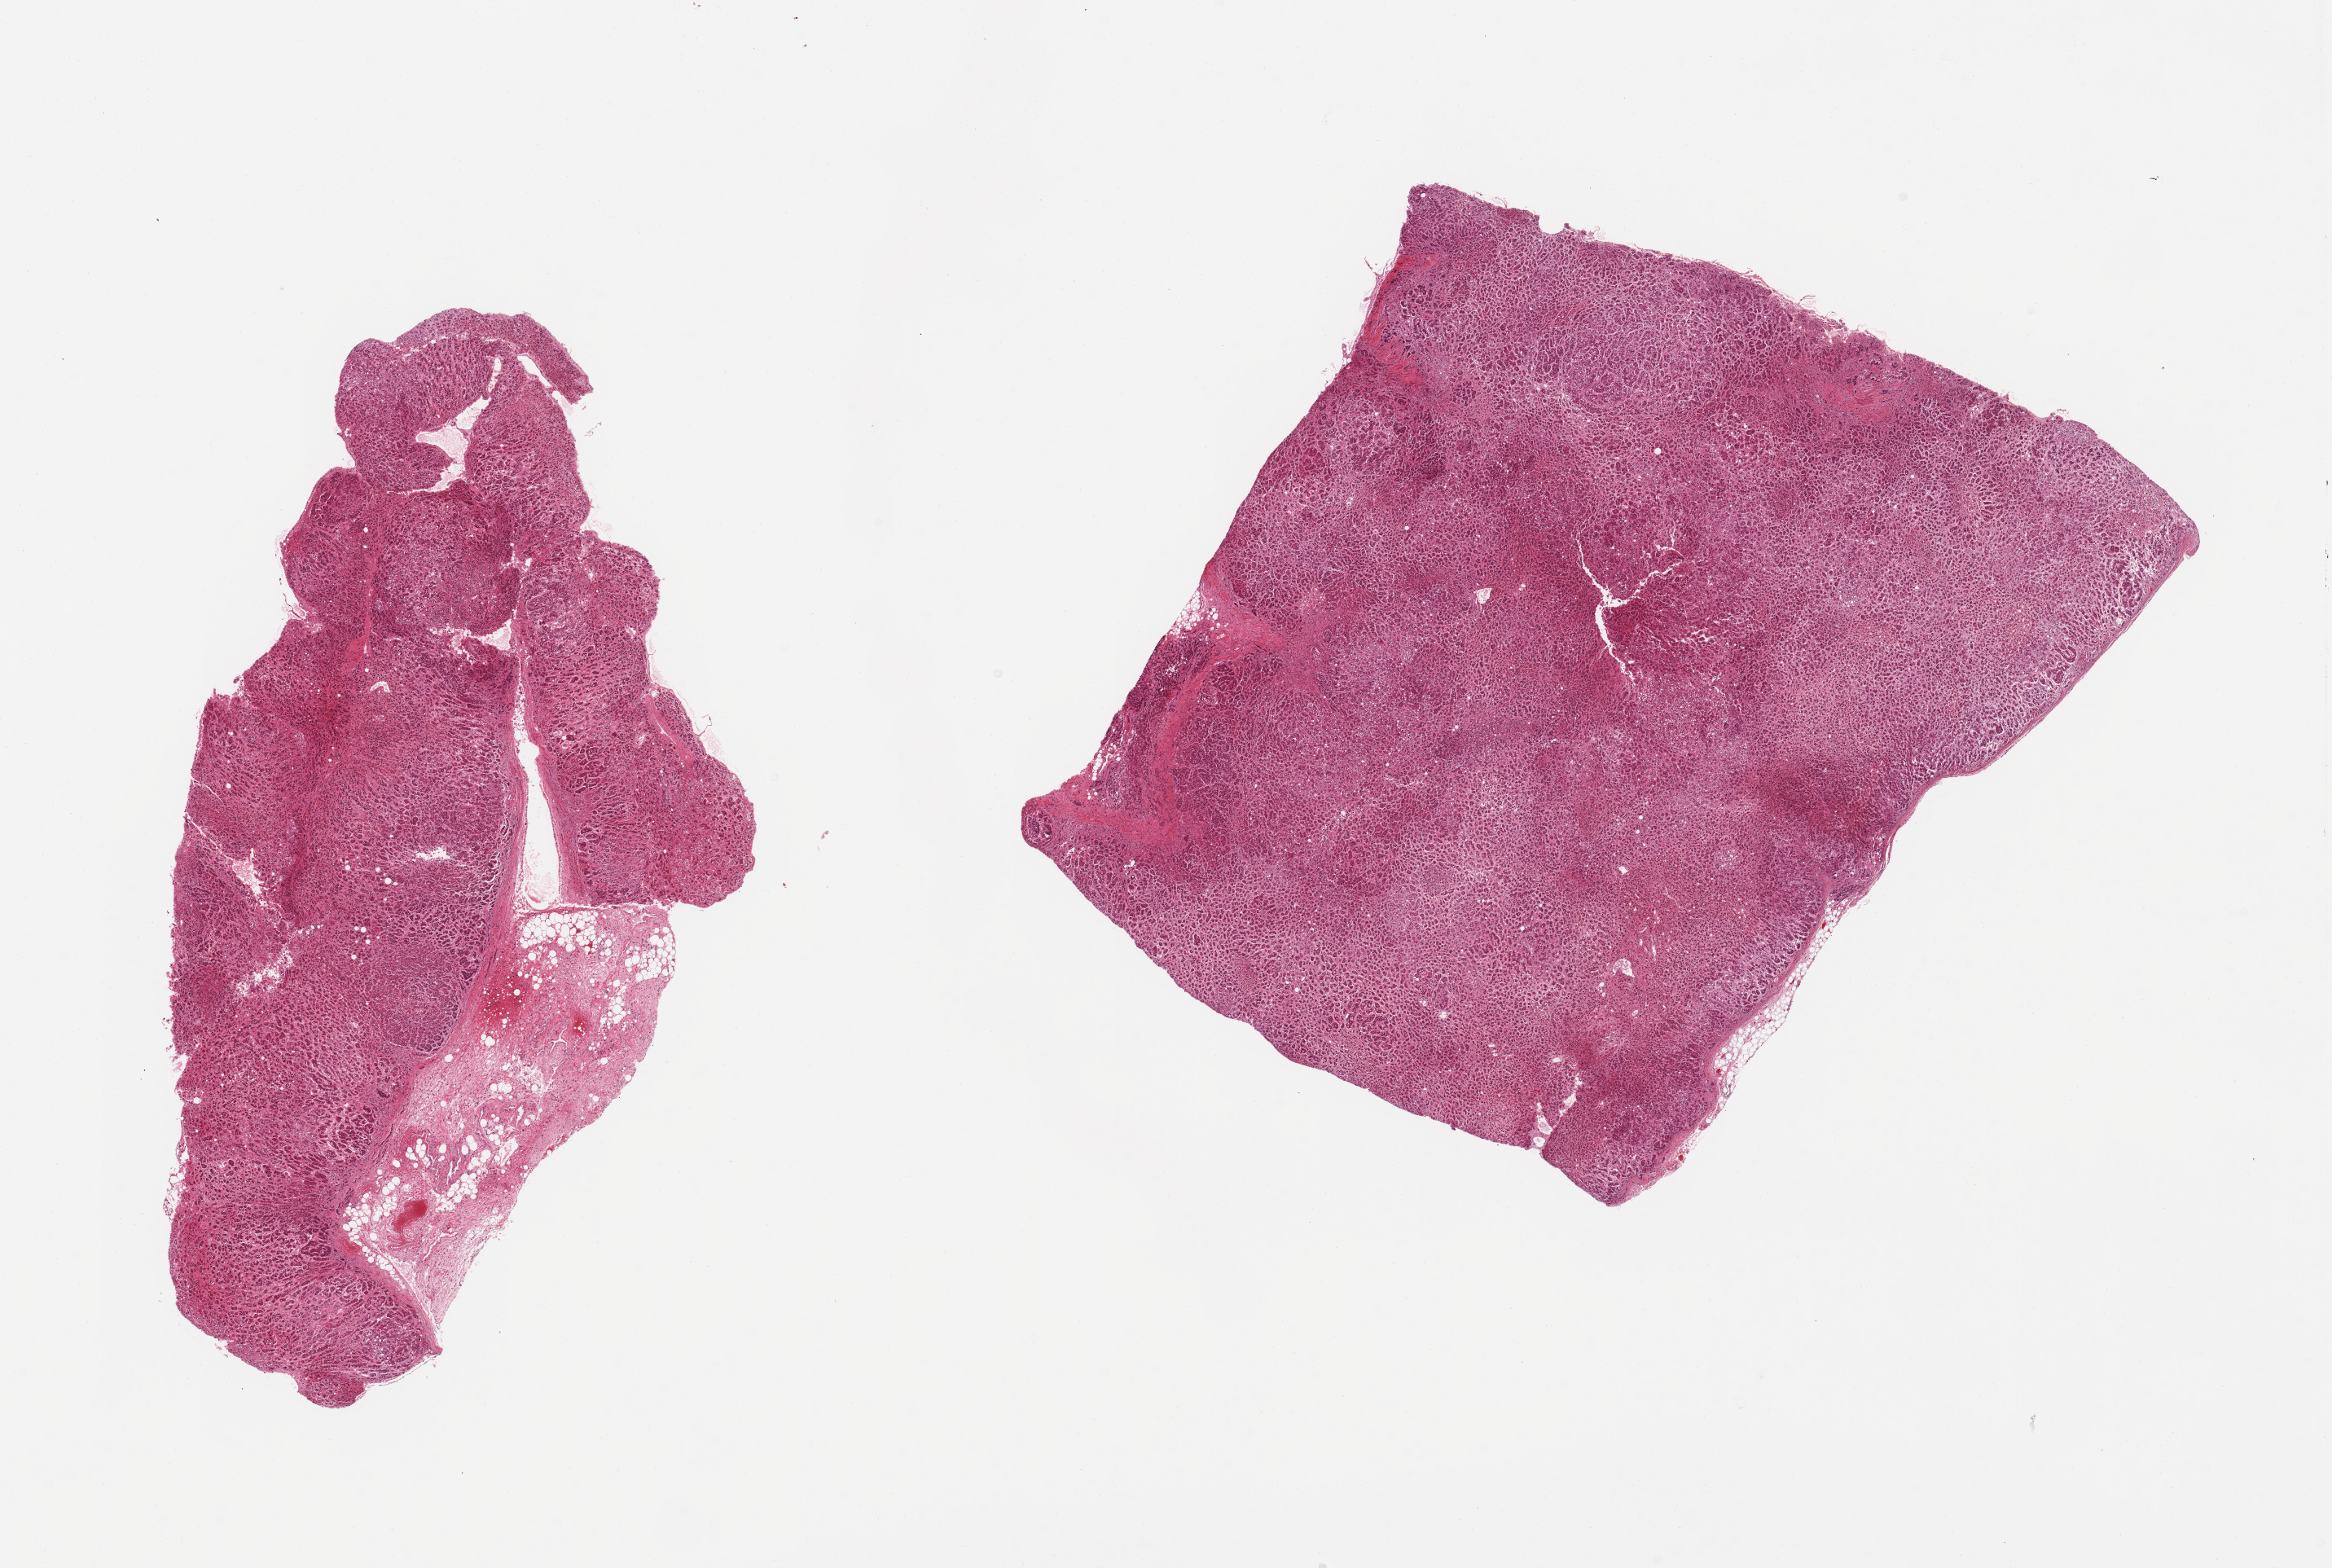
Whole-slide image, H&E stain, whole scanned area (about 22.6 x 15.2 mm) shown as a low-resolution overview; PAXgene-fixed, paraffin-embedded tissue; target tissue: adrenal gland; donor tissue sample.
Review note (as recorded): 2 pieces; 1 piece includes 20% attachment of fat.